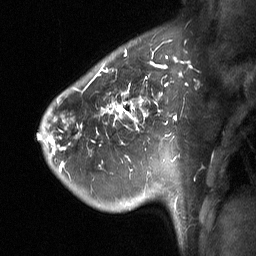
Breast MRI (dynamic contrast-enhanced), one sagittal slice; dynamic contrast-enhanced study with each time point stored as its own series, time point 2 of 3 at this slice position (early post-contrast, ordered by acquisition time); 1.5 T; TE 4.8 ms, TR 27 ms; 2 mm slice thickness; 256 × 256 image matrix, field of view 200 × 200 mm. Patient: female, 42 years. From the clinical record (not read from this slice): setting: breast cancer imaged before/during neoadjuvant chemotherapy; receptor status: triple-negative.
Structures marked on this image (semi-automatic segmentation, software-assisted and operator-edited):
- analysis volume of interest (the breast-tissue region the enhancement analysis was run in; not a lesion): bounding box (x1, y1, x2, y2) in pixels: (49, 45, 197, 197)
- tumour enhancement mask (voxels above the 90 % enhancement threshold inside the analysis volume of interest): (51, 55, 189, 169)